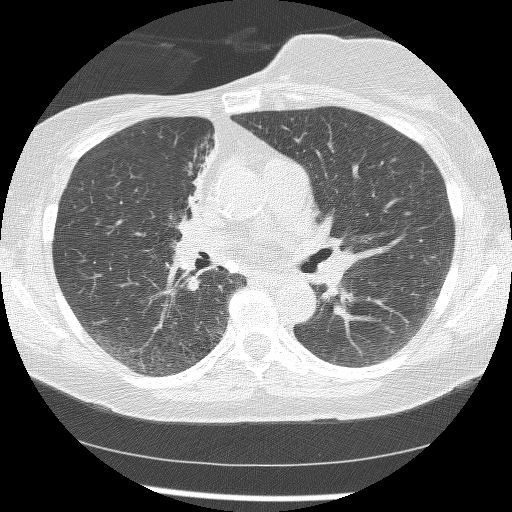
Axial slice from a low-dose chest CT screening exam, baseline screening round, lung window (W 1500 / L -600 HU), 2.5 mm slice thickness, 512 × 512 image matrix. Female participant, aged 56 years at enrolment. Current smoker at enrolment.
Expert reader's lesion annotation, box from (x=159, y=128) to (x=214, y=252) px. The screening reader recorded 2 non-calcified nodules or masses ≥4 mm on this exam; which of them this box marks is not recorded. Later outcome: lung cancer diagnosed 1185 days after this screen — adenocarcinoma, NOS, right upper lobe, stage IIIB (AJCC 6th edition), 8 mm at pathology.